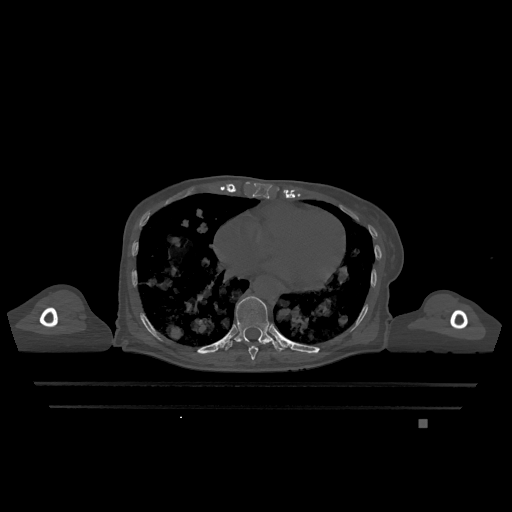
CT including the spine, one axial slice. Position 661 of 1317 along the scan axis. Bone window (W 1800 / L 400 HU). 0.5 mm slice thickness. 512 × 512 image matrix, field of view 500 × 500 mm. Female patient, age 74 years. Case-level facts recorded for this patient, not image findings: primary cancer: lung.
Annotated regions visible in this slice (semi-automatic segmentation, software-assisted and operator-edited):
- T10 vertebra: bounding box [x1, y1, x2, y2] px = [225, 296, 283, 353]
- T9 vertebra: [248, 346, 258, 361]